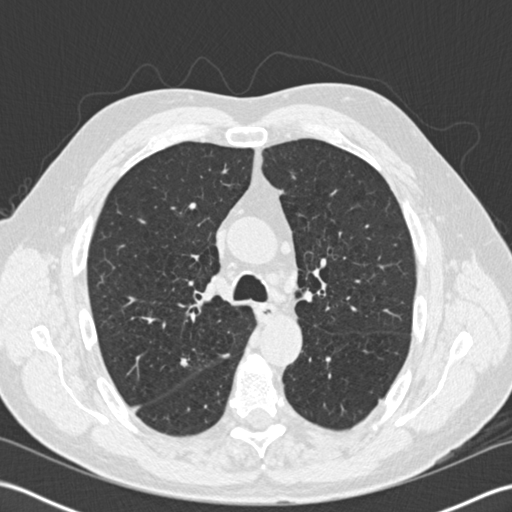
Axial slice from a low-dose chest CT screening exam; second annual screen; lung window (W 1500 / L -600 HU); standard (soft-tissue) reconstruction kernel (B30f); slice 59 of 204 in the series; 512 × 512 image matrix, field of view 350 × 350 mm. Male, age 65 years at enrolment. Former smoker at enrolment.
Lesion marked by an expert reader, bounding box [x1, y1, x2, y2] px = [159, 343, 205, 384]. The screening reader recorded 6 non-calcified nodules or masses ≥4 mm on this exam (right upper lobe, left upper lobe, left upper lobe, right upper lobe, left upper lobe, right upper lobe); which of them this box marks is not recorded. Later outcome: lung cancer diagnosed 421 days after this screen (after the third annual screen) — adenocarcinoma, NOS, right upper lobe, moderately differentiated (G2), stage IA (AJCC 6th edition), 16 mm at pathology.